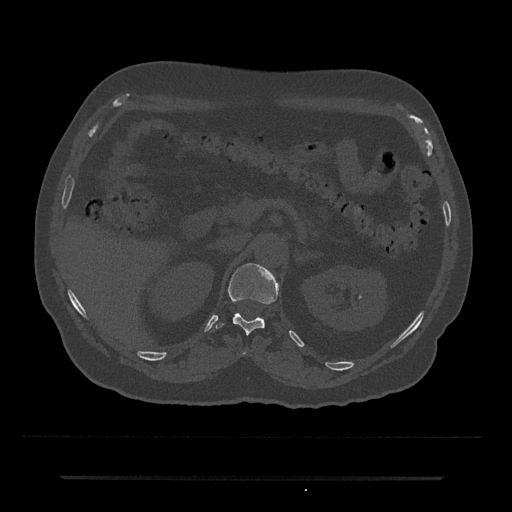
CT including the spine, one axial slice; position 123 of 797 along the scan axis; reconstruction kernel Br40s/3; 120 kVp; bone window (W 1800 / L 400 HU); 512 × 512 image matrix, field of view 437 × 437 mm. Patient: male, 69 years. Case-level facts recorded for this patient, not image findings: primary cancer: prostate.
Outlined on this slice (semi-automatic segmentation, software-assisted and operator-edited):
- T11 vertebra: bounding box [x1, y1, x2, y2] px = [242, 352, 247, 355]
- T12 vertebra: [215, 264, 279, 334]